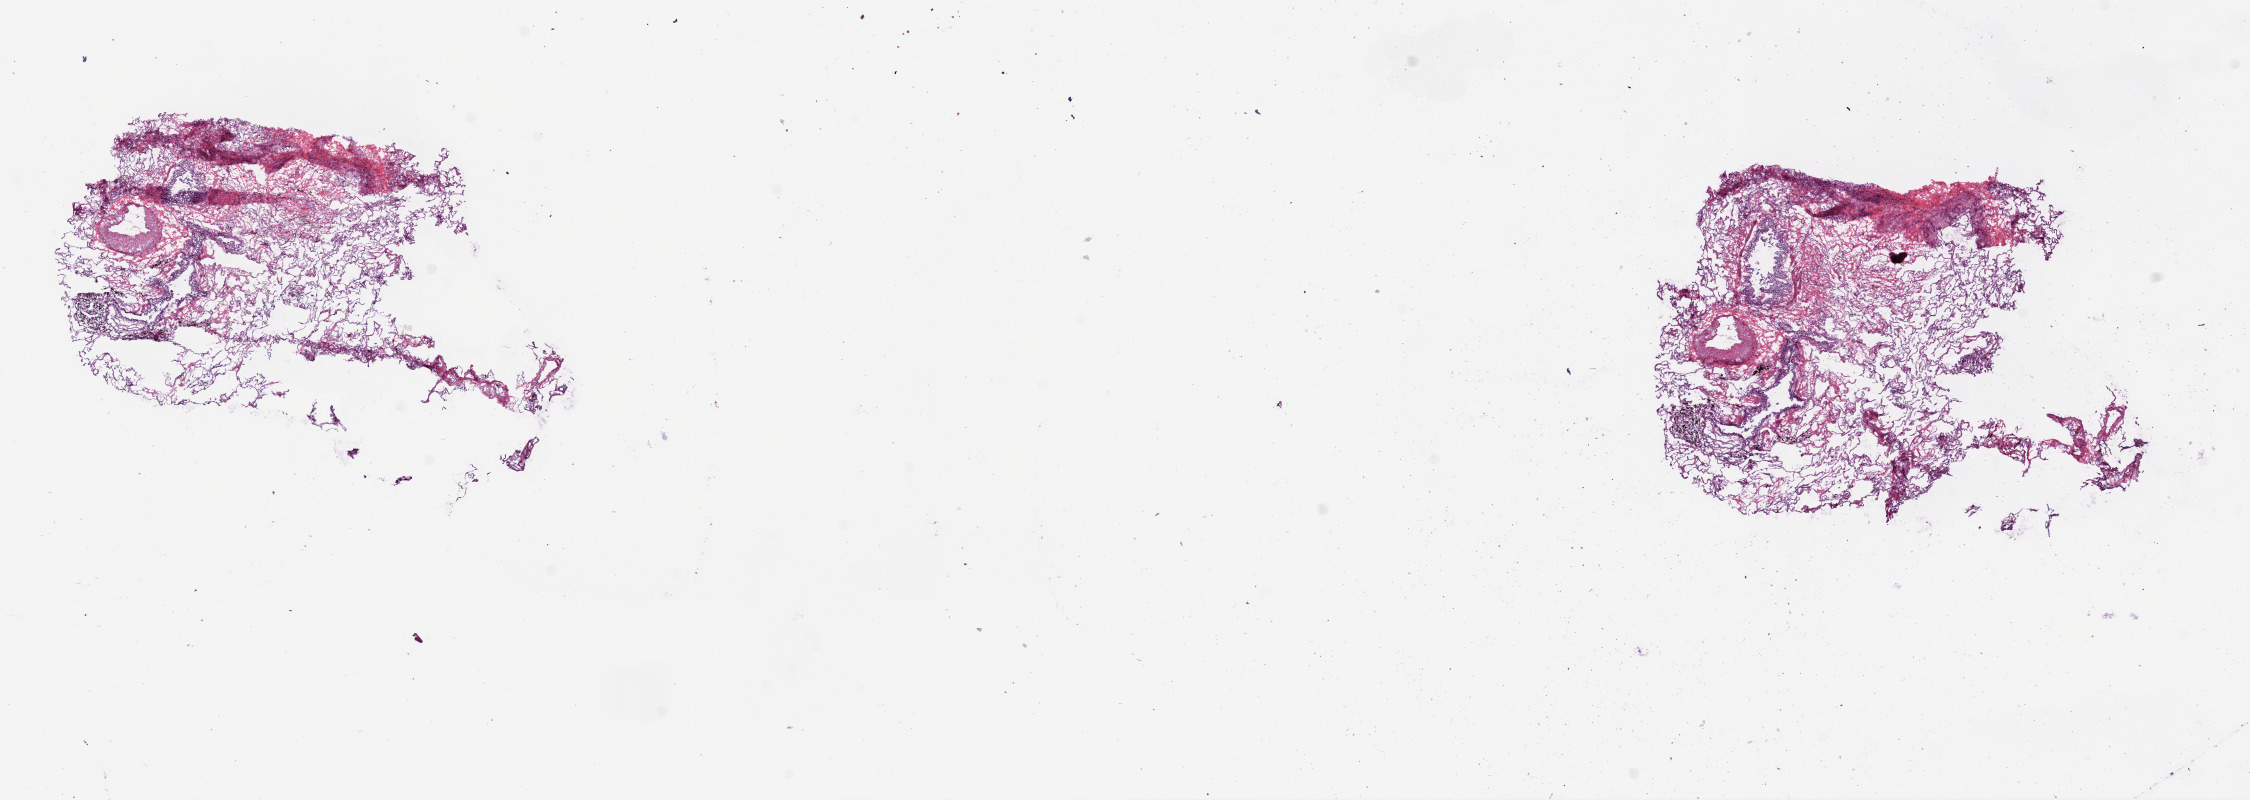
Whole-slide histology image, Hematoxylin and eosin (H&E) stained — whole scanned area (about 18.1 x 6.4 mm) shown as a low-resolution overview, frozen section, sample: solid tissue normal (non-tumour tissue), lung. Male, age 74 years at initial diagnosis.
This section: solid tissue normal sample (biorepository sample class). Patient diagnosis: Basaloid squamous cell carcinoma (upper lobe, lung).